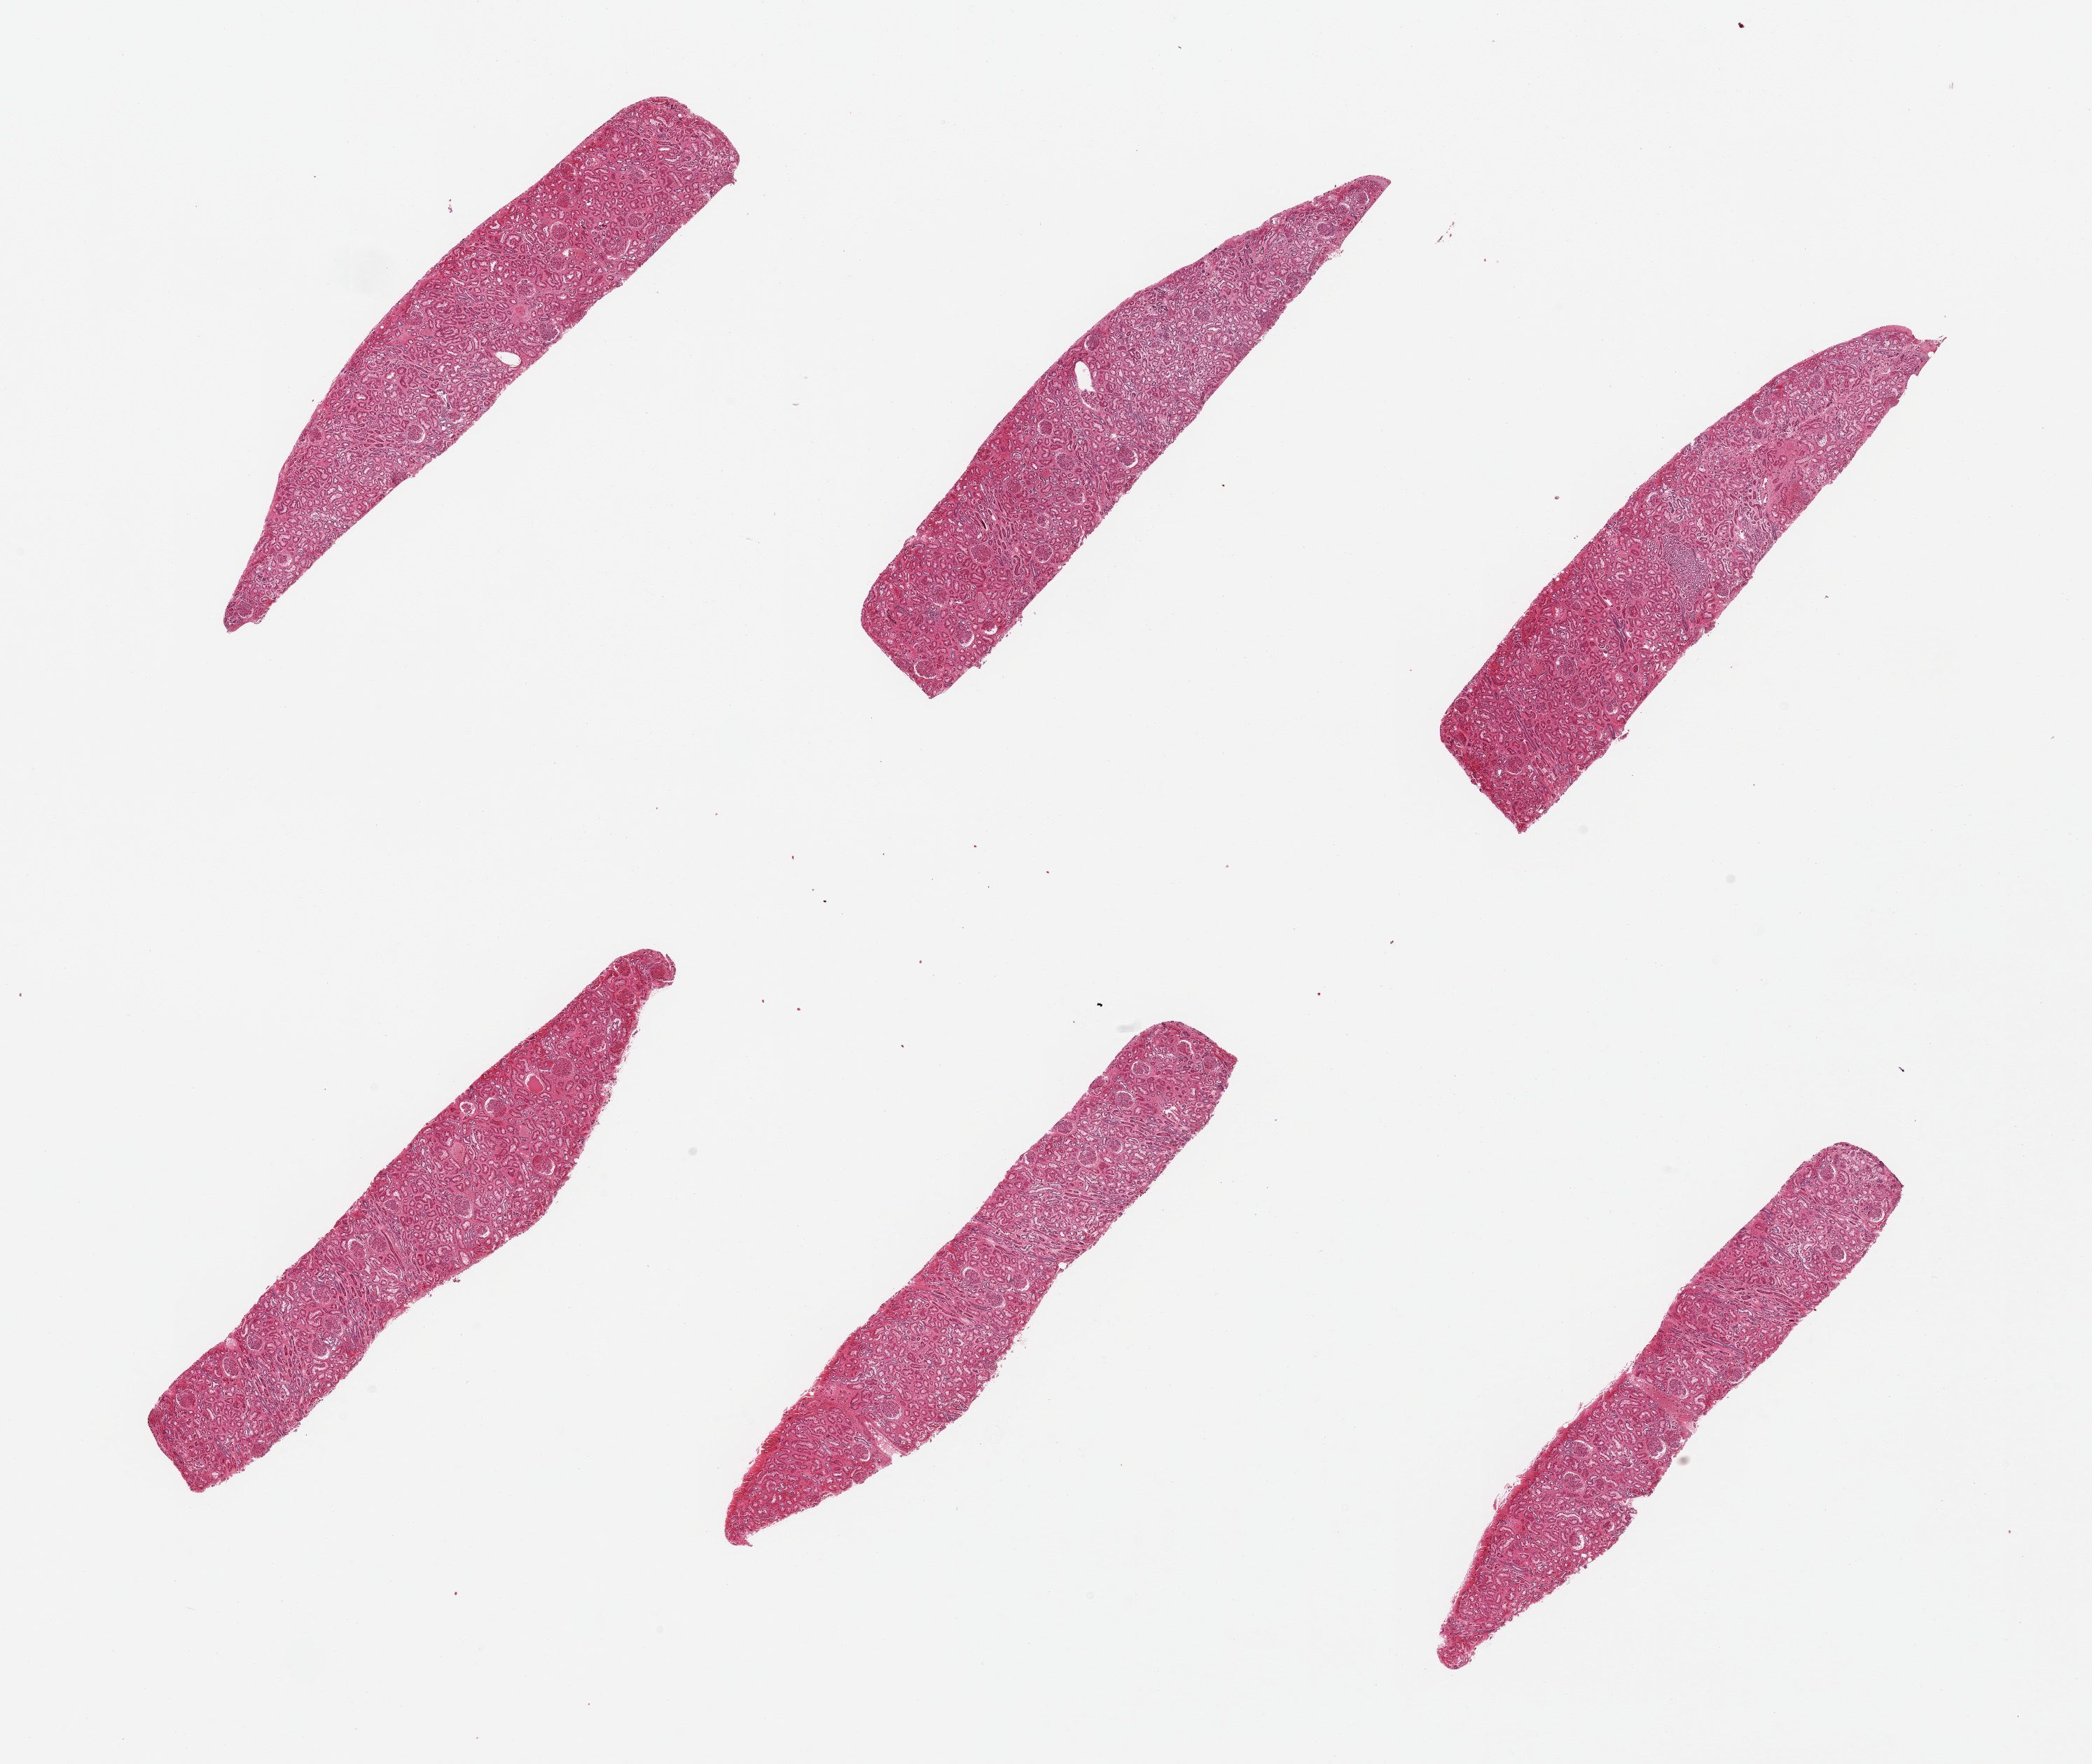
Digitized haematoxylin and eosin-stained section, shown as a low-resolution overview of the whole scanned area (about 23.6 x 19.9 mm), PAXgene-fixed paraffin-embedded (PFPE) section, sampled site (target tissue): renal cortex, tissue donor sample.
- review note (as recorded): 6 pieces; no chronic or active lesion